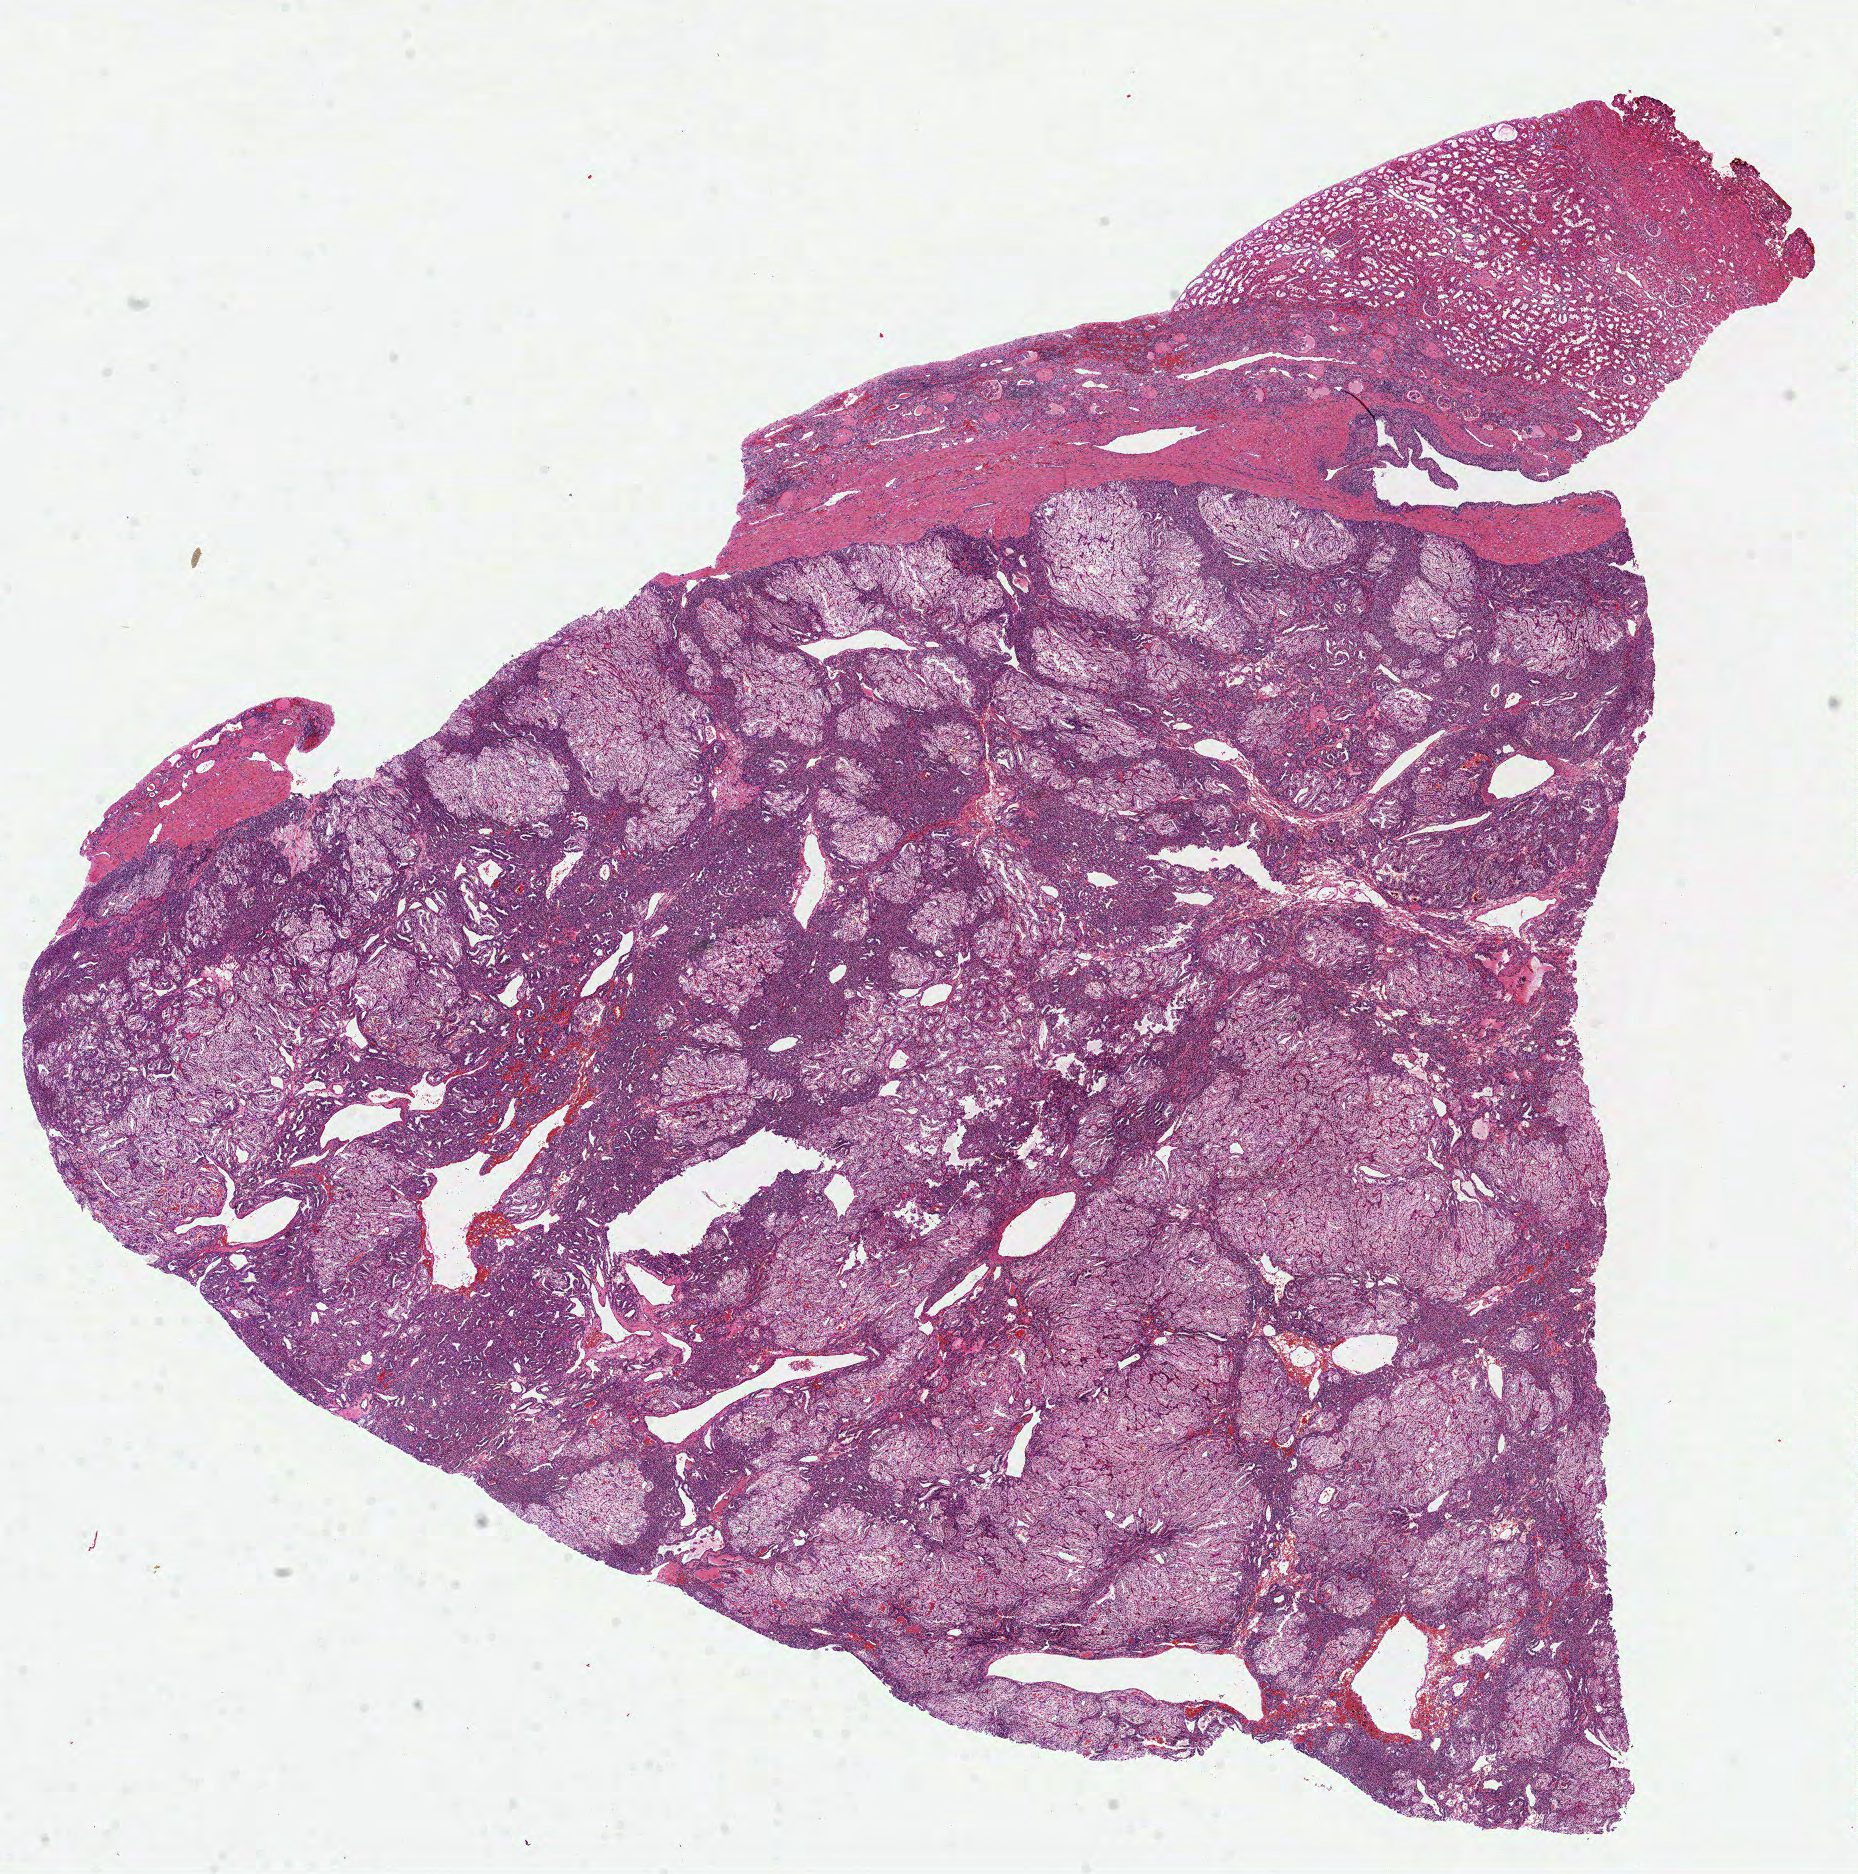
Whole-slide histology image, H&E-stained — whole scanned area (about 15.0 x 15.1 mm) shown as a low-resolution overview; formalin-fixed paraffin-embedded (FFPE) diagnostic section; sample: primary tumour, kidney. Patient: male, age at initial diagnosis 62 years. Histologic grade: G2 (moderately differentiated).
TNM: T1 N0 M0. AJCC pathologic stage: I. Diagnosis: Clear cell adenocarcinoma, NOS.